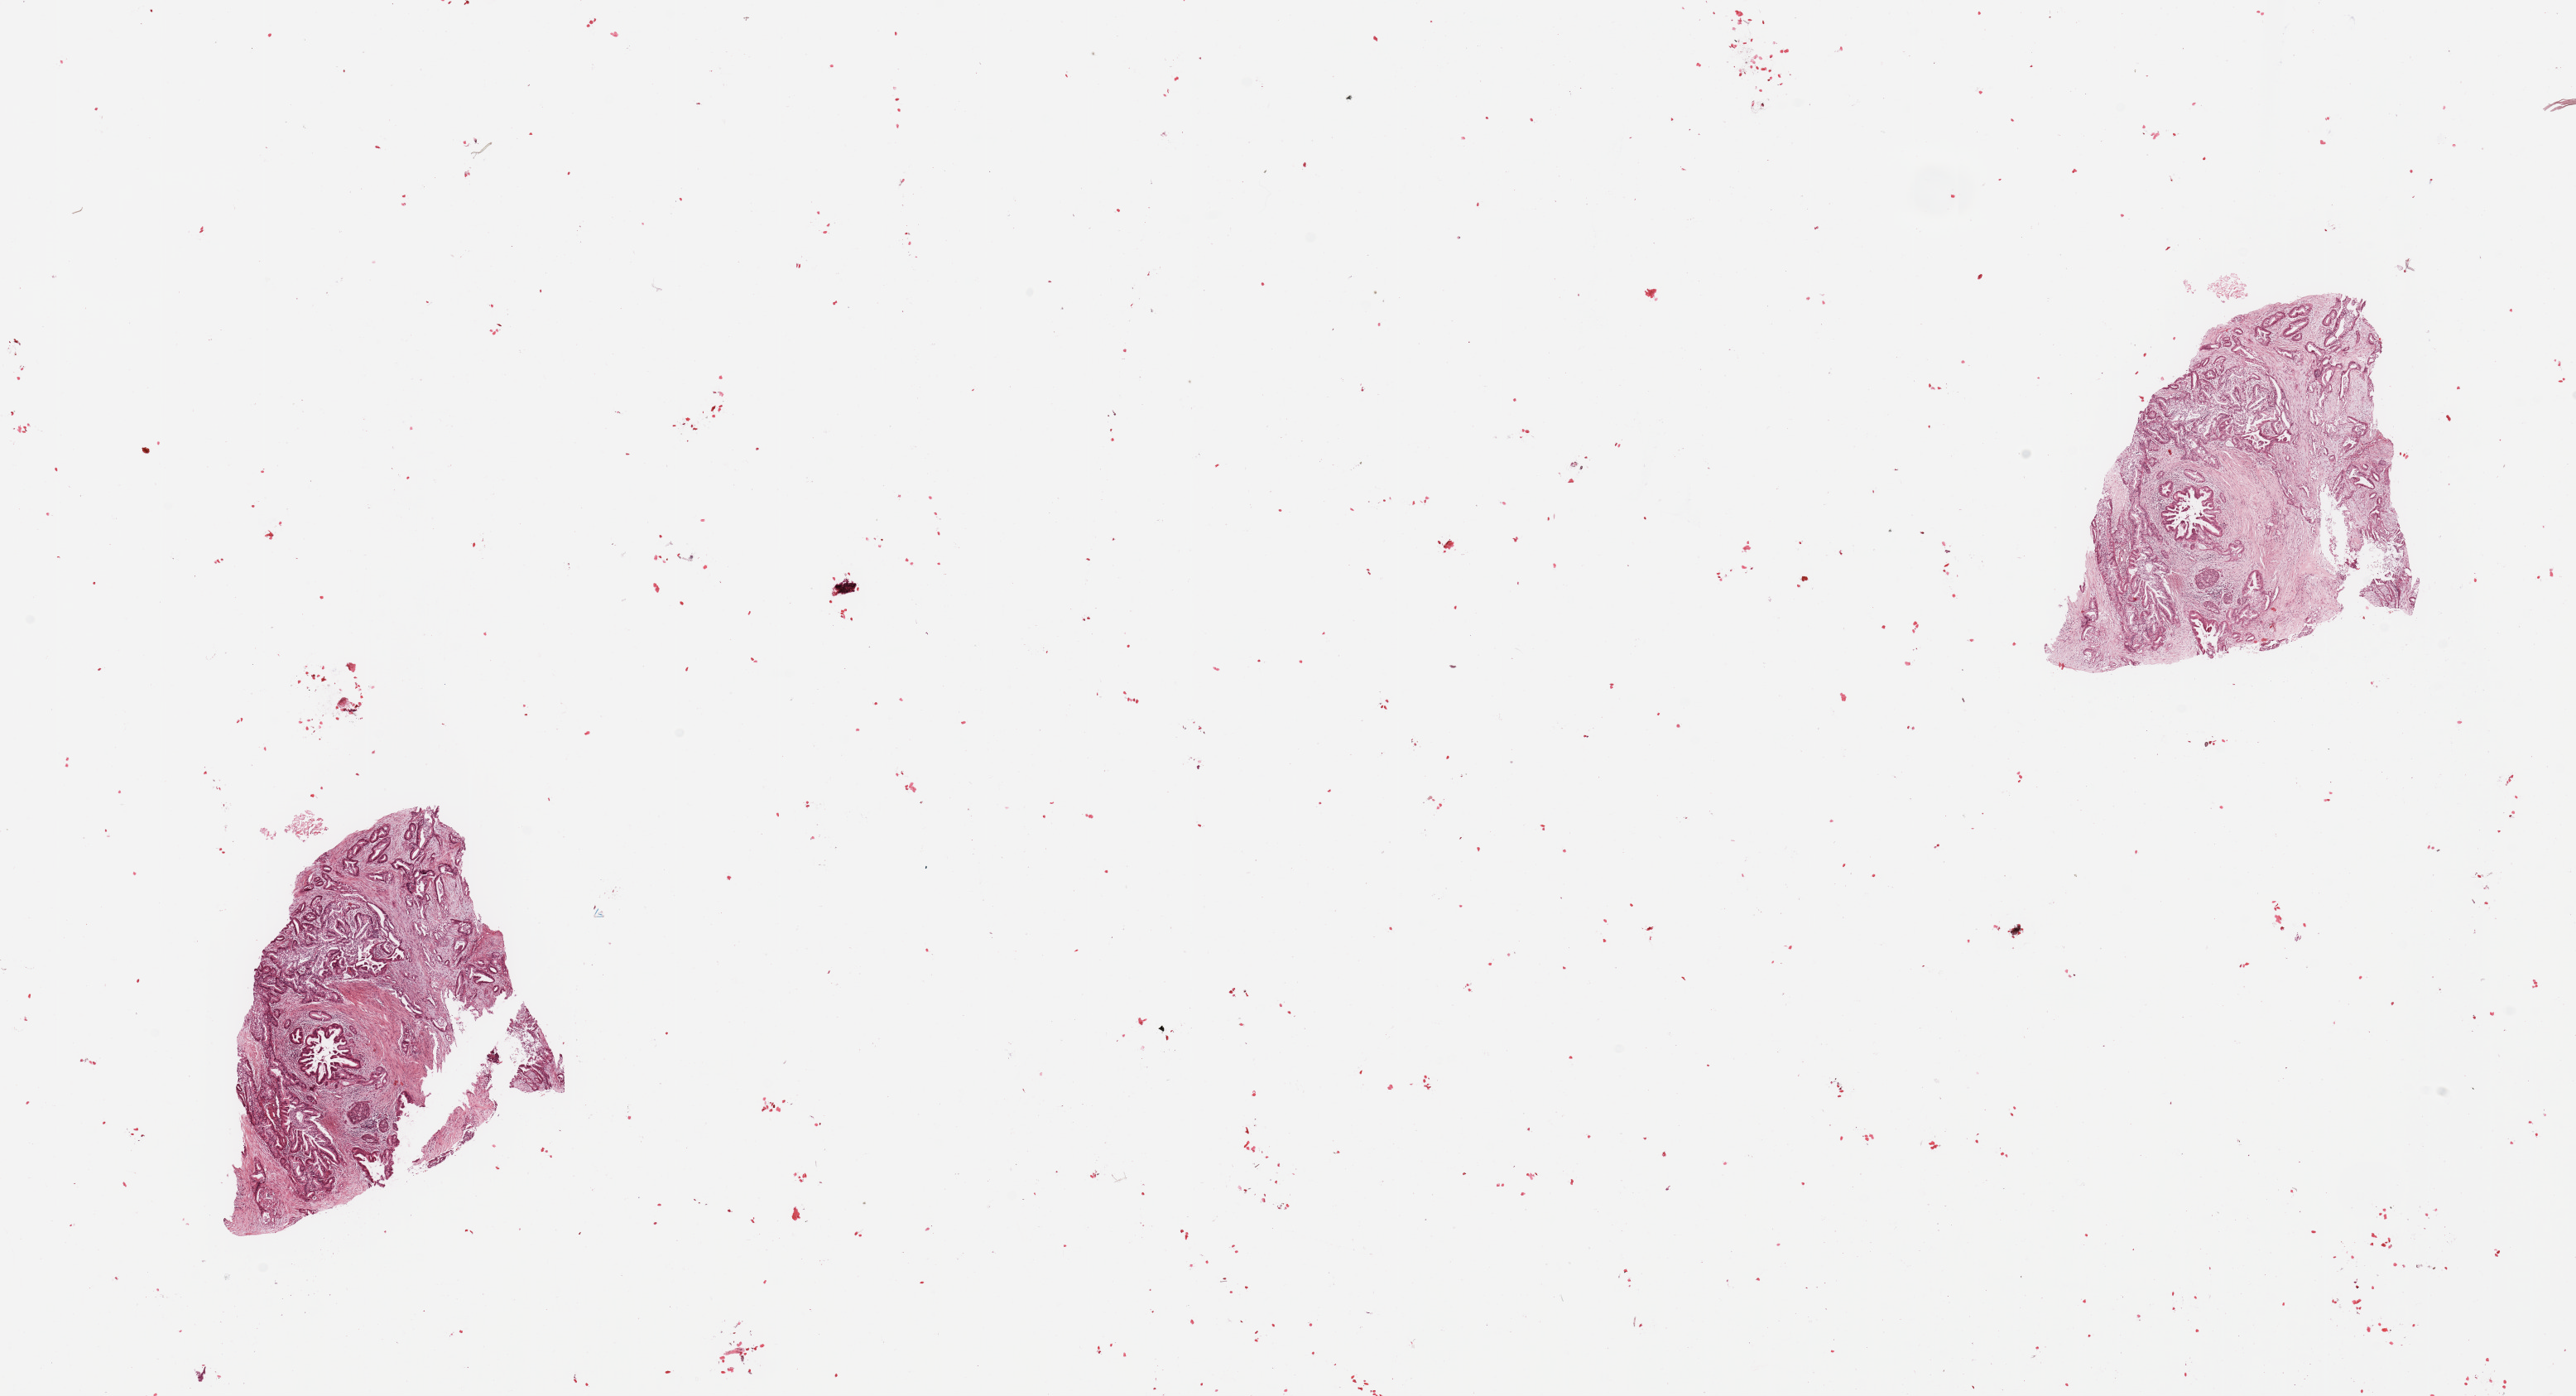
Digitized H&E-stained tissue section (whole slide), low-resolution overview of the scanned area, about 24.6 x 13.3 mm. Tumour tissue sample, sampled site: pancreas. Female, 45 y/o. Histologic grade: G2 (moderately differentiated). Composition of this section per pathologist review: tumour nuclei 30%, necrosis 2%.
Diagnosis: Infiltrating duct carcinoma, NOS. AJCC pathologic stage: IIB. Primary tumour site (as recorded): head.